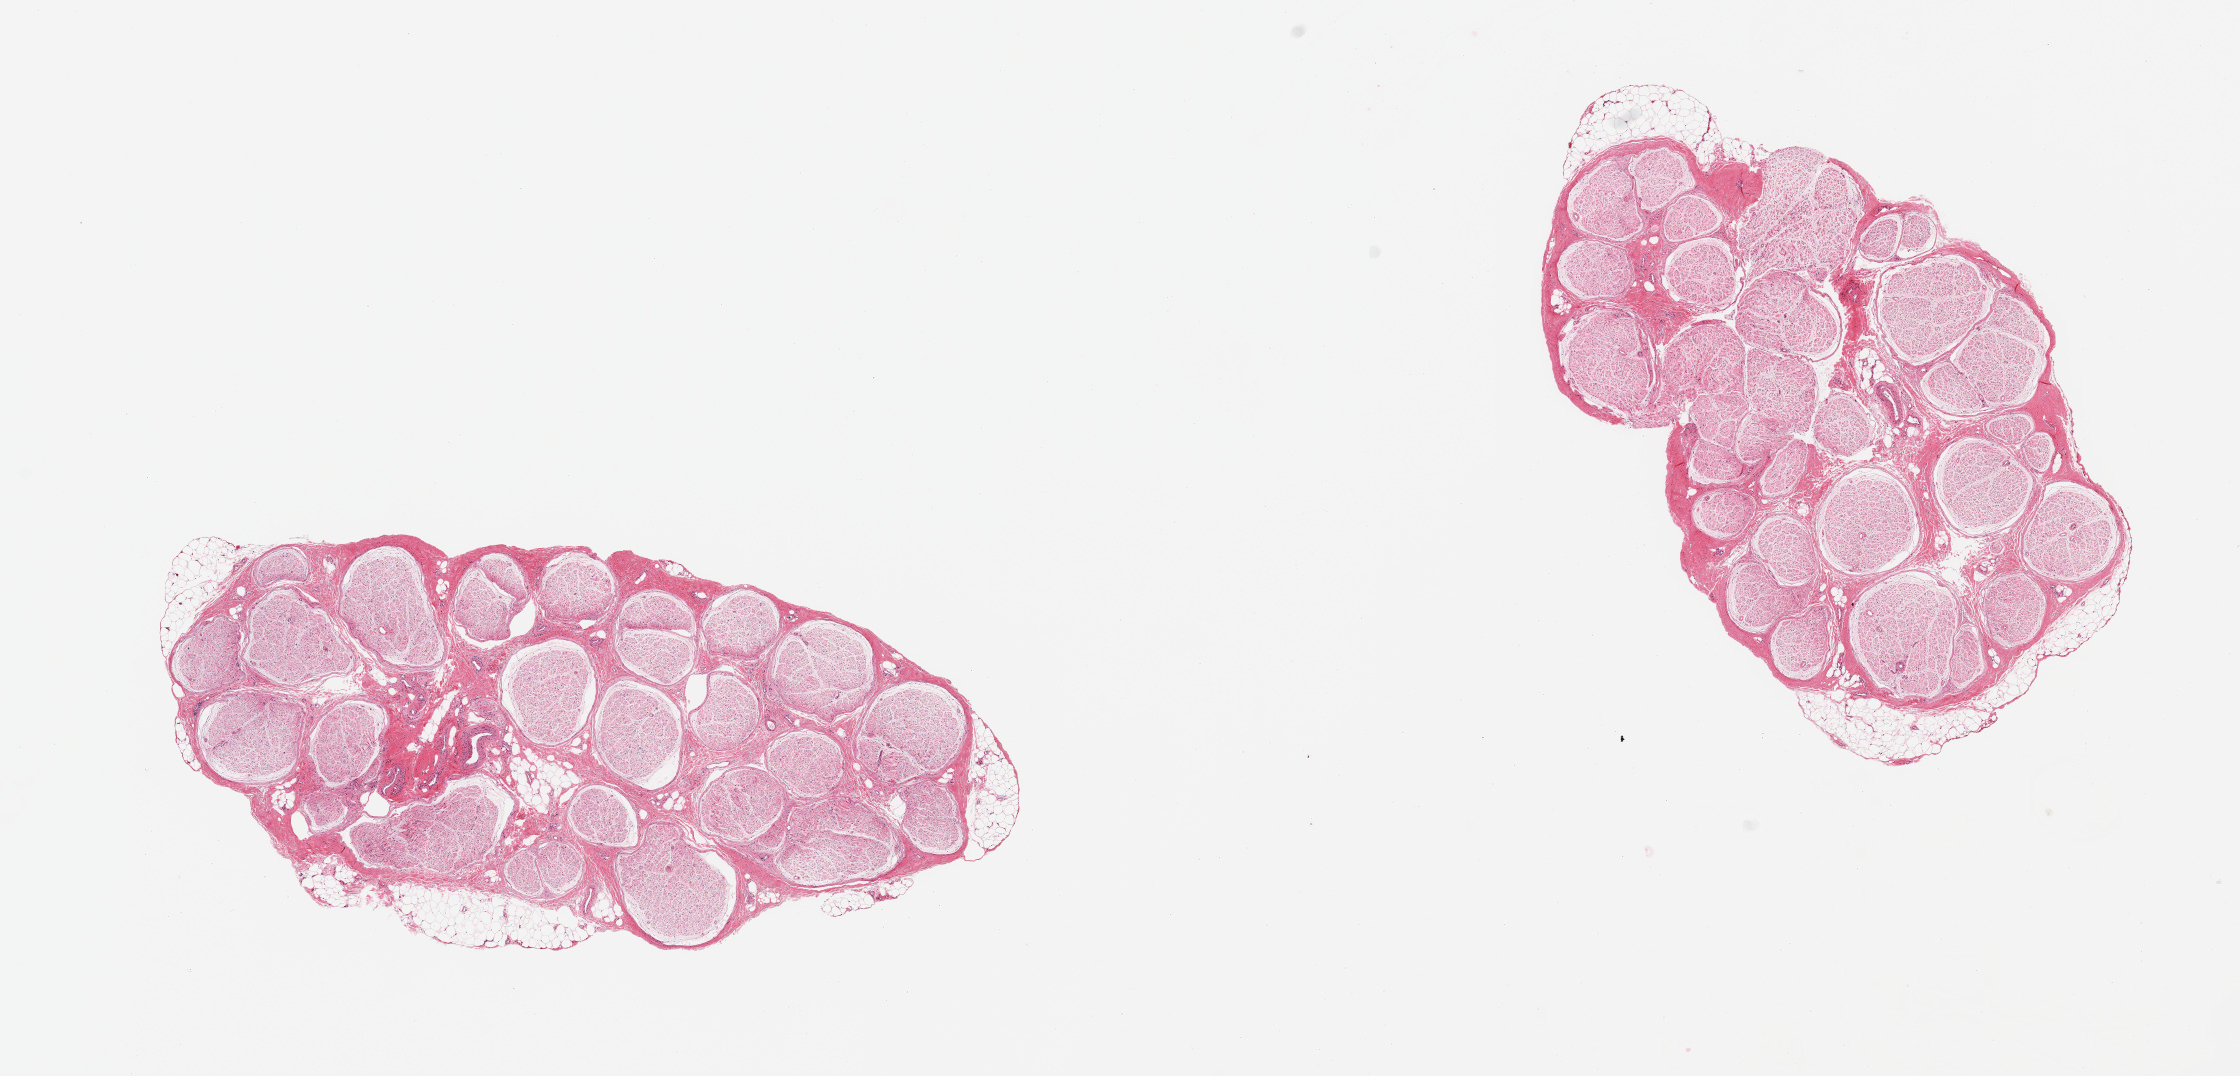
Digitized hematoxylin and eosin (H&E)-stained section, low-resolution overview of the scanned area, about 17.7 x 8.5 mm, PAXgene-fixed paraffin-embedded (PFPE) section, sampled site (target tissue): tibial nerve, donor tissue sample. Donor: female.
Review note (as recorded): 2 pieces.